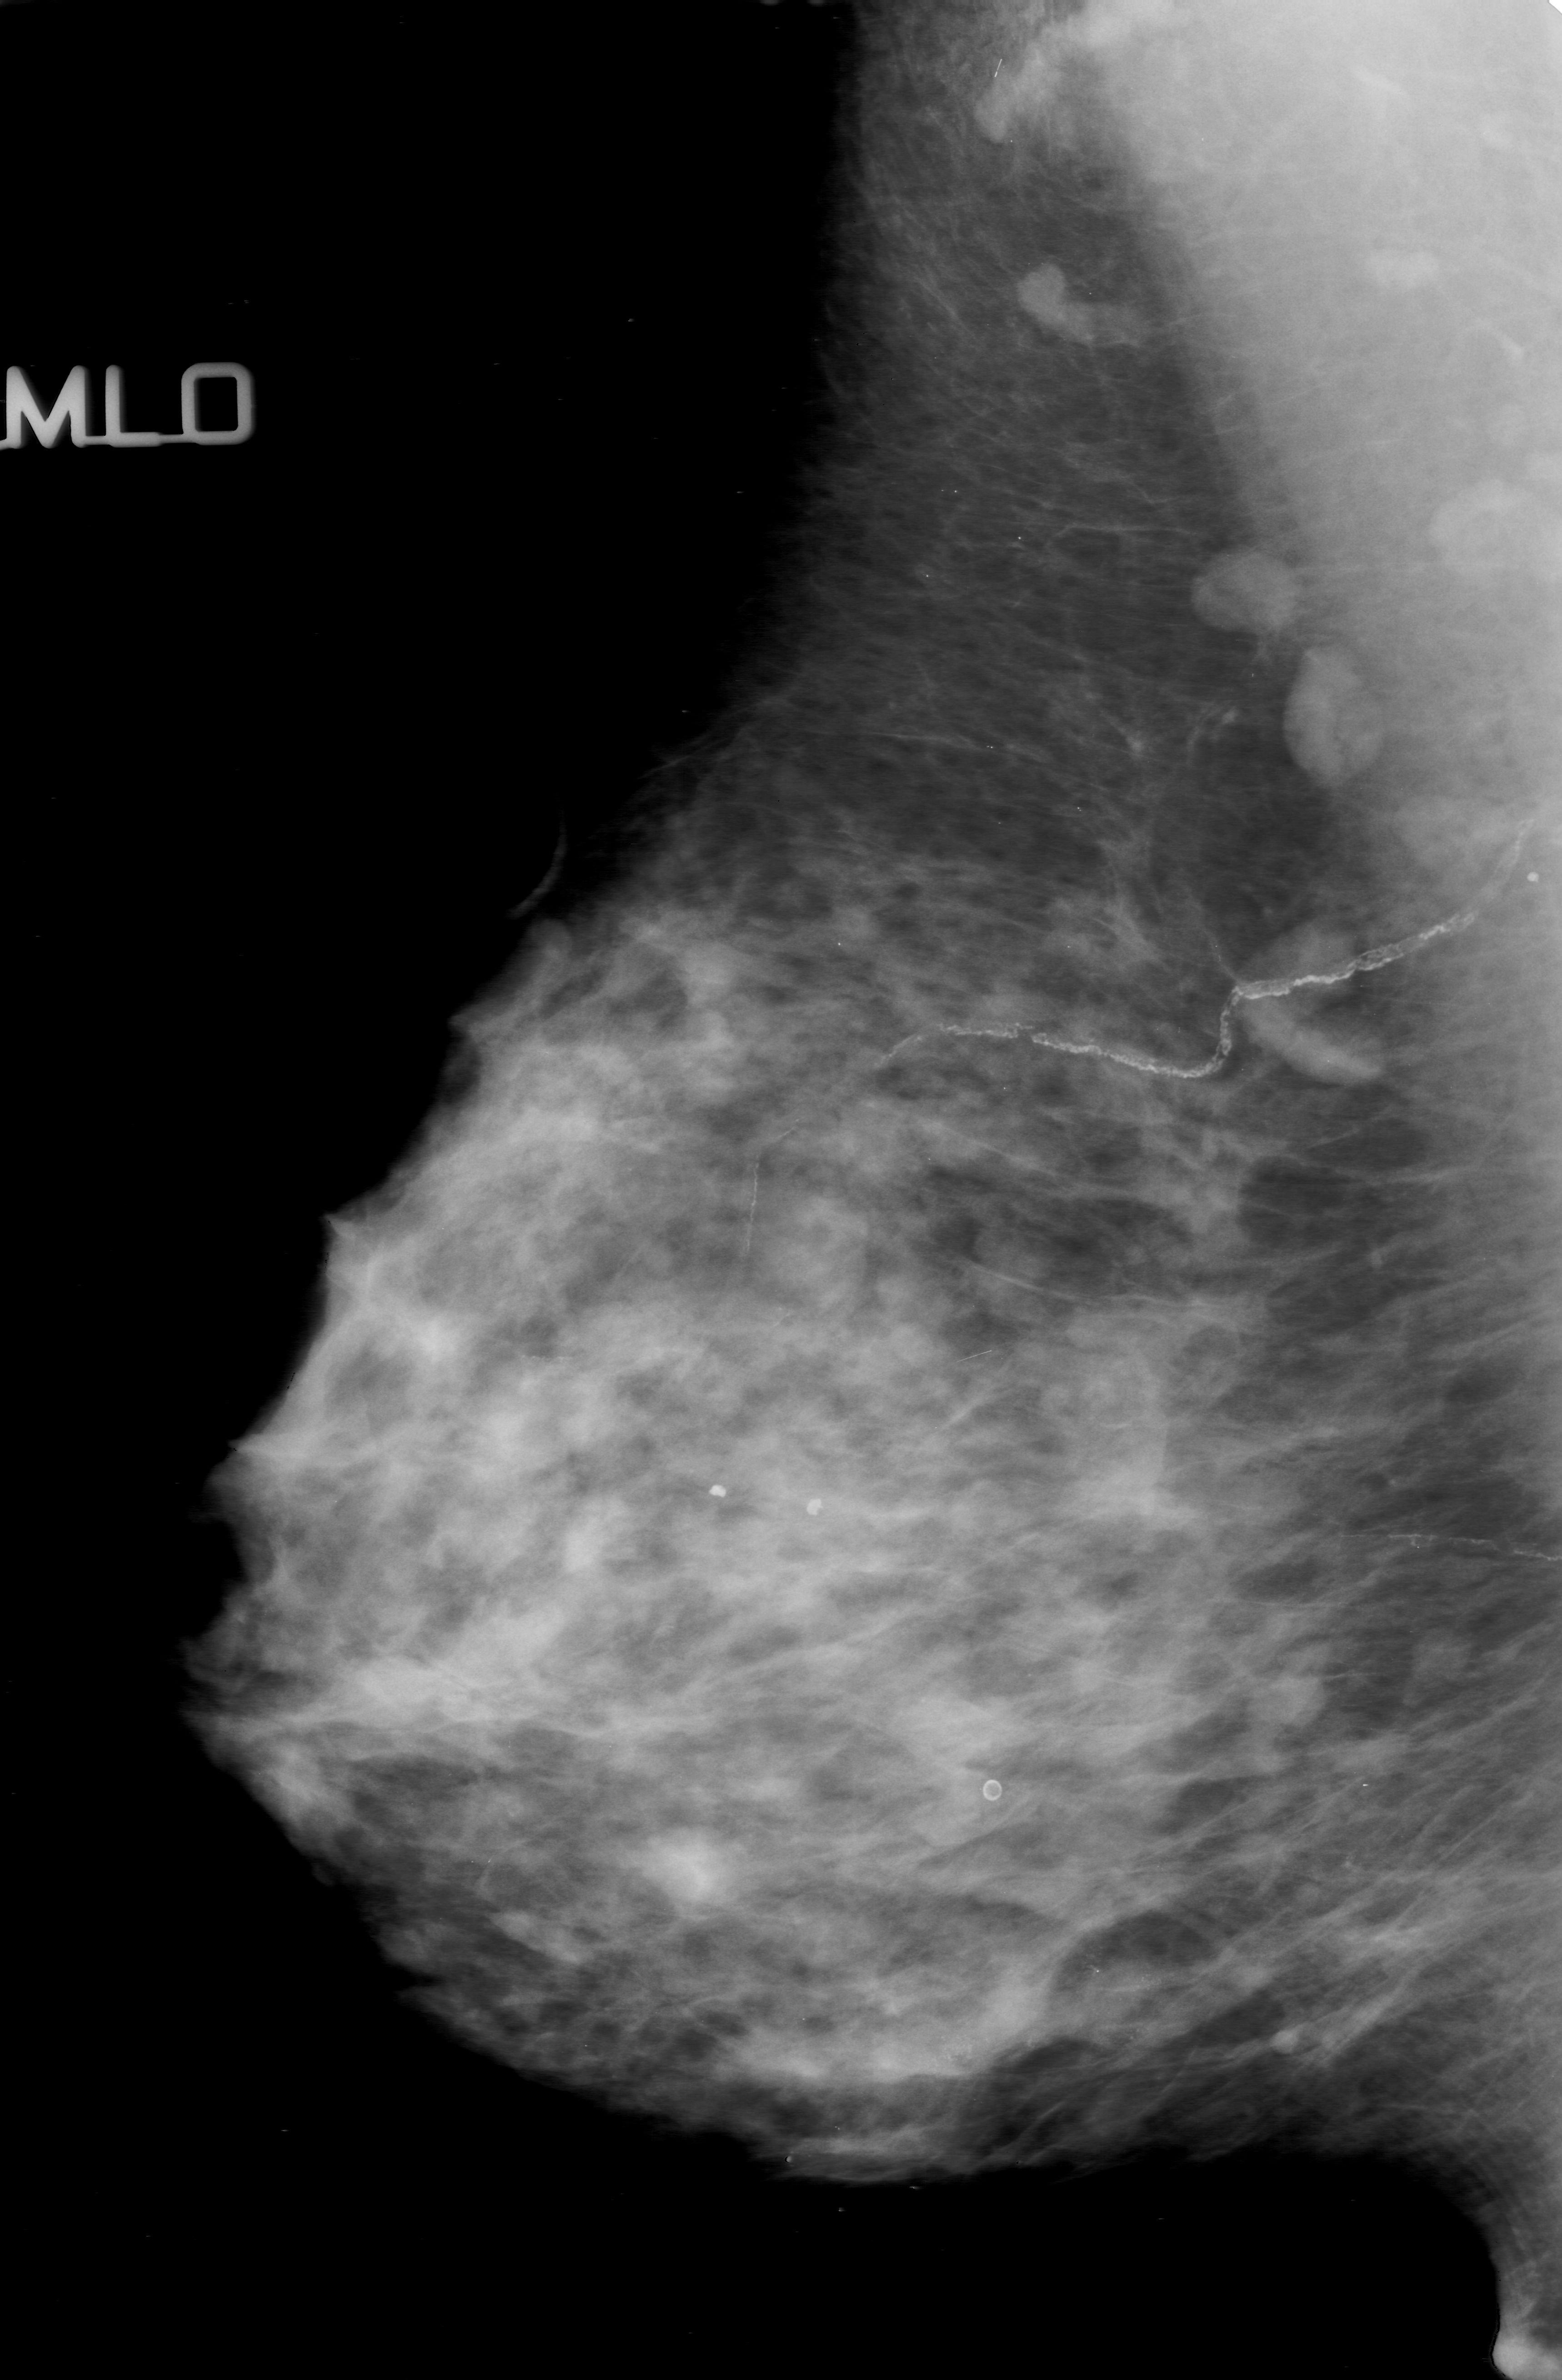
Digitized screen-film mammogram; right breast; MLO view; breast composition: heterogeneously dense (BI-RADS density category 3 of 4).
- Finding: calcifications, morphology amorphous, distribution segmental; BI-RADS assessment category 5; subtlety rating 3 on a 1 (subtle) to 5 (obvious) scale; pathology (as recorded): malignant.